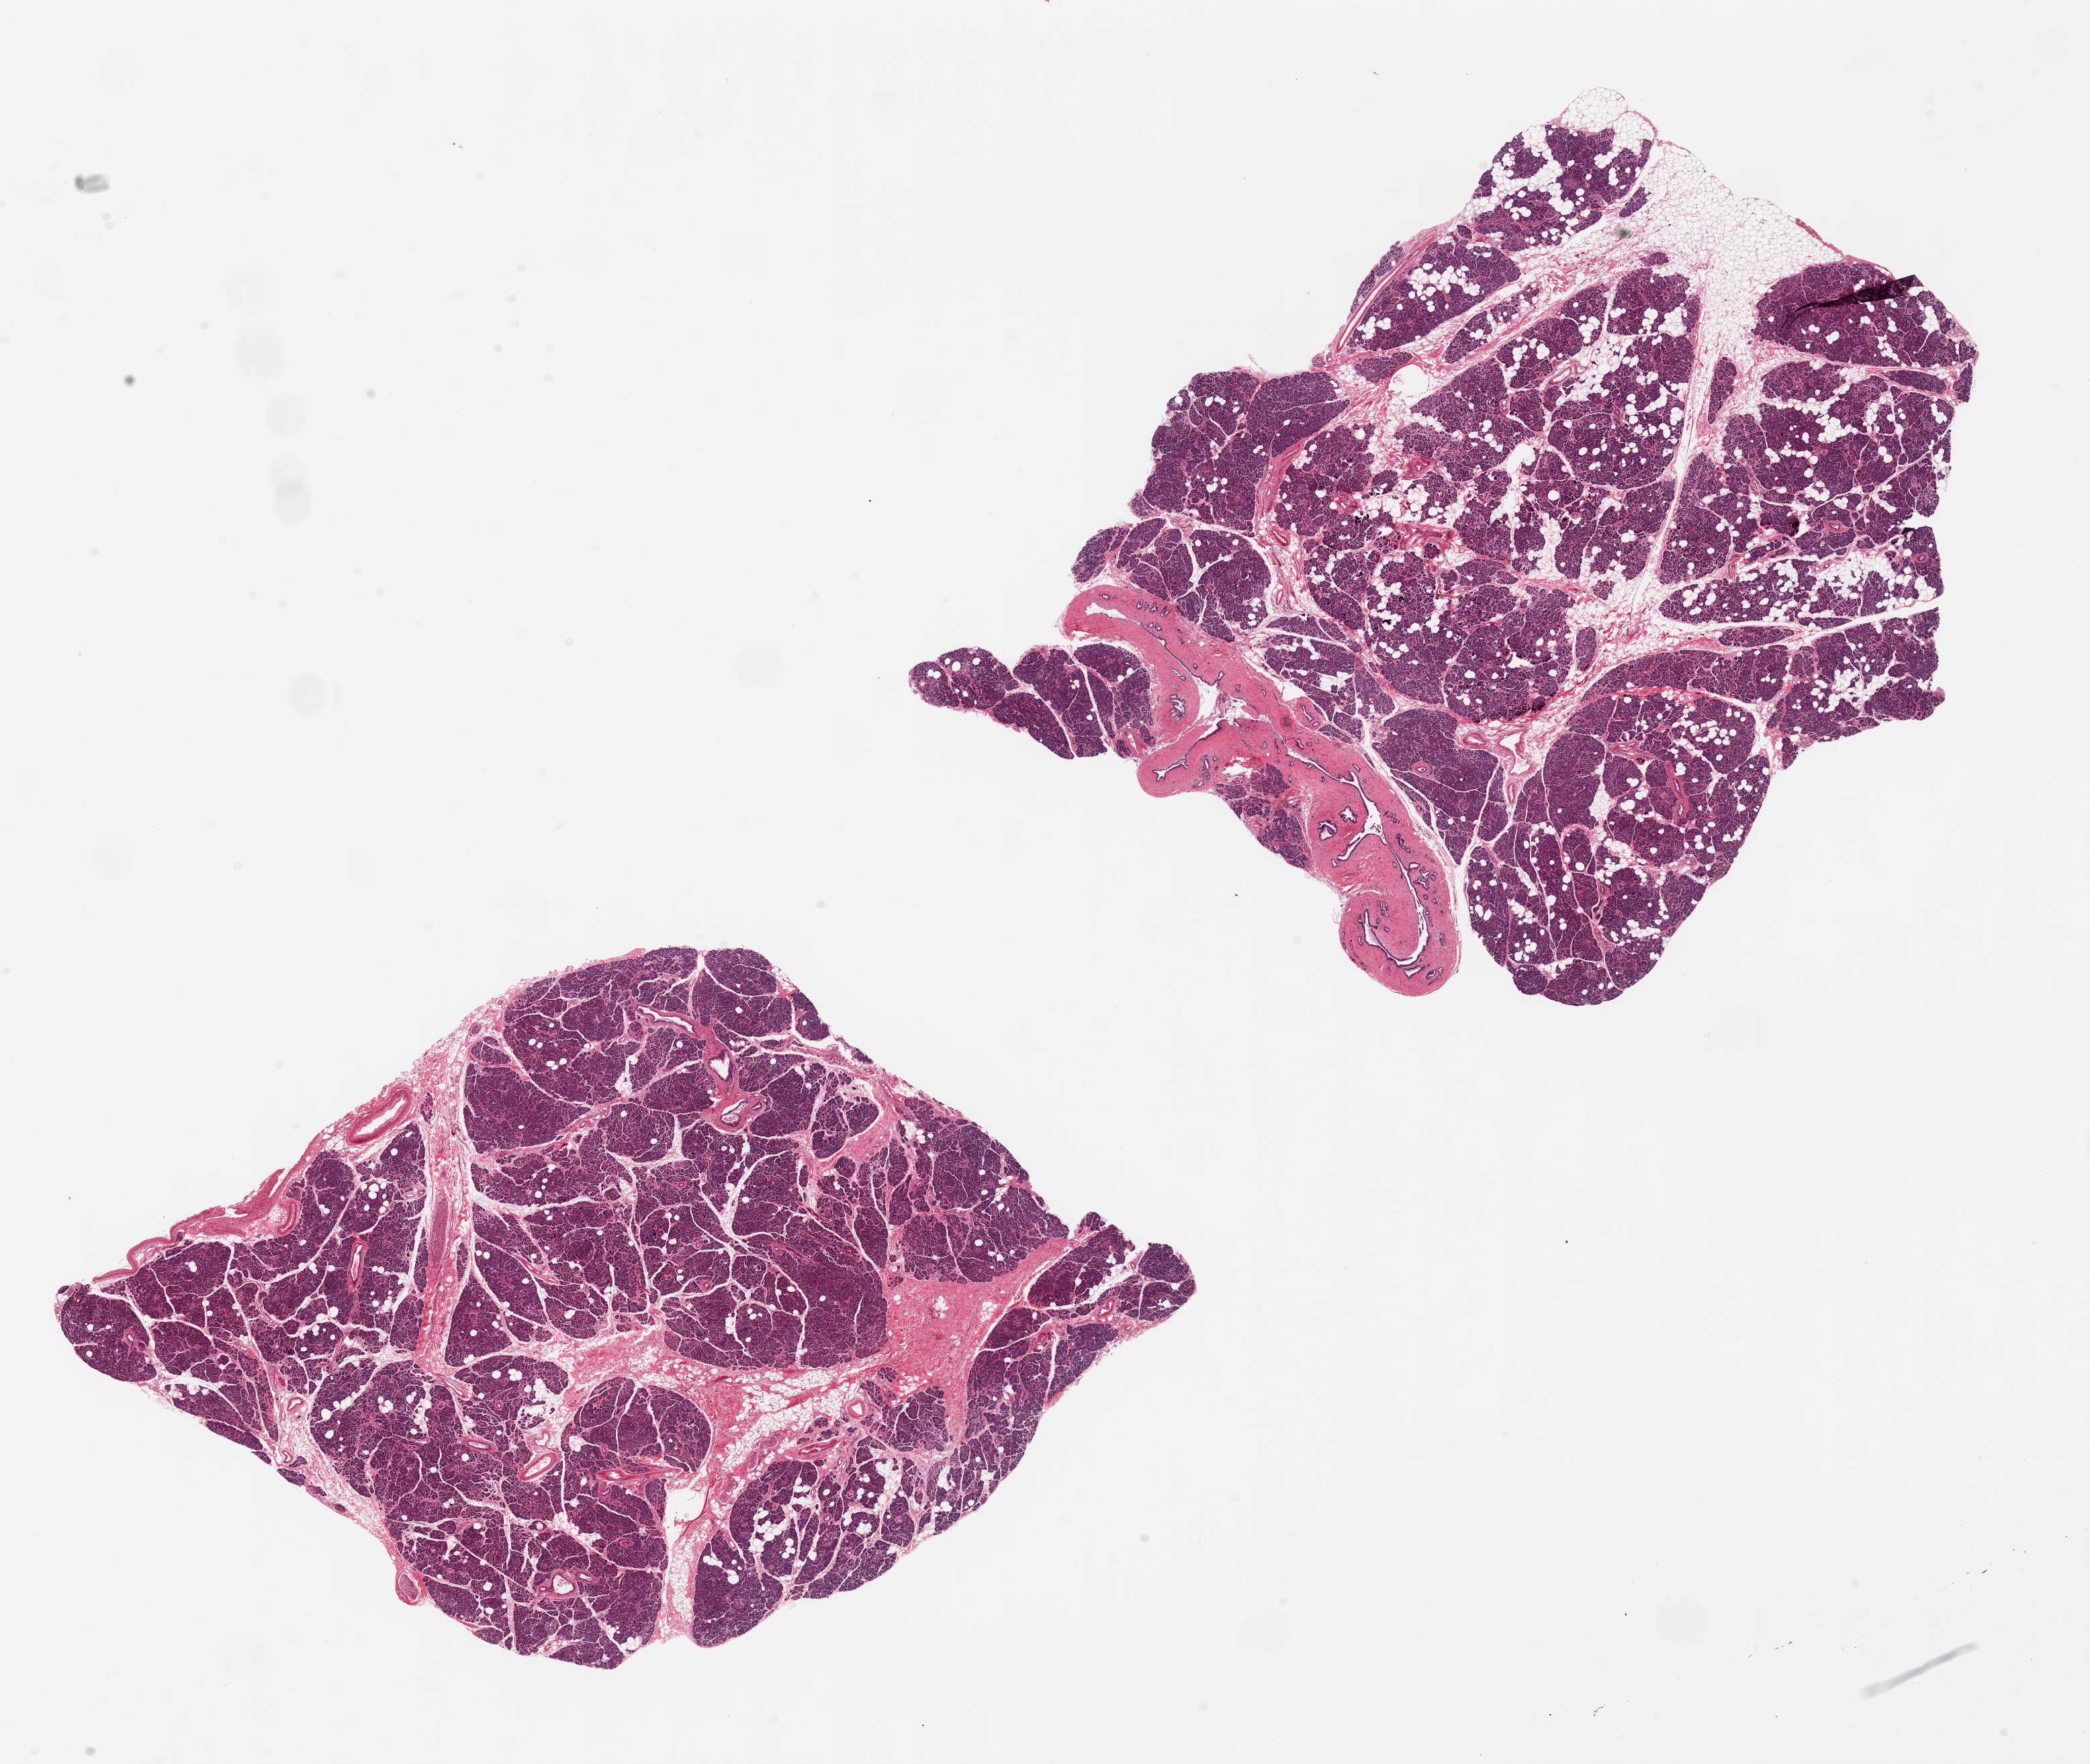
Digitized haematoxylin and eosin-stained section, shown as a low-resolution overview of the whole scanned area (about 24.6 x 20.8 mm, acquisition: 20x scan); PAXgene-fixed, paraffin-embedded tissue; target tissue: pancreas; donor tissue sample. Female donor.
Reviewer comment on this tissue sample: 2 pieces, 10x9 & 11x10mm; islets reasonably well-preserved.